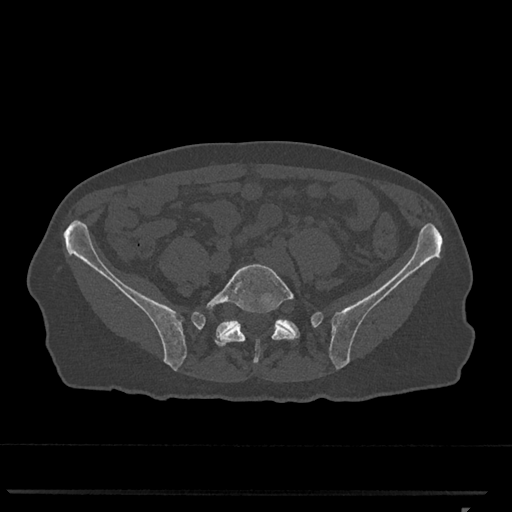
CT including the spine, one axial slice. Slice 138 of 793 in the series (ordered by position). Bone window (W 1800 / L 400 HU). 0.5 mm slice thickness. 512 × 512 image matrix, field of view 380 × 380 mm. Female patient, age 62 years. Case-level facts recorded for this patient, not image findings: primary cancer: renal.
Outlined on this slice (semi-automatically segmented with operator editing):
- L5 vertebra: bounding box [x1, y1, x2, y2] px = [206, 264, 296, 363]